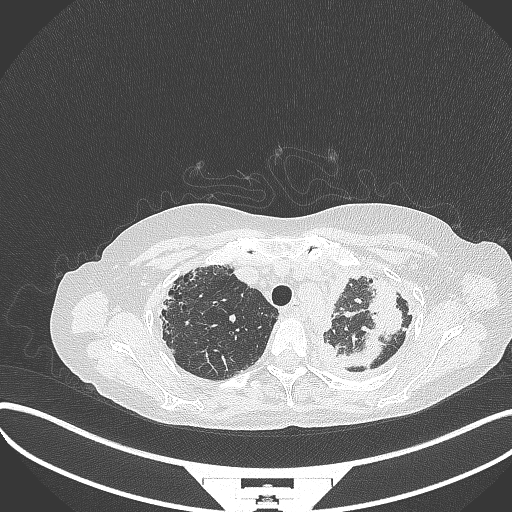
Chest CT, one axial slice. Reconstruction kernel B70f. 120 kVp. Lung window (W 1500 / L -600 HU). 1 mm slice thickness. 512 × 512 image matrix, field of view 400 × 400 mm. Patient: female, 56 years. From the clinical record (not read from this slice): clinical TNM (as recorded): T1 N0 M0.
Structures marked on this image (rectangle marked by the reading radiologist):
- lung tumour (recorded histology: adenocarcinoma): bounding box <343,273,402,366> (left, top, right, bottom; pixels)